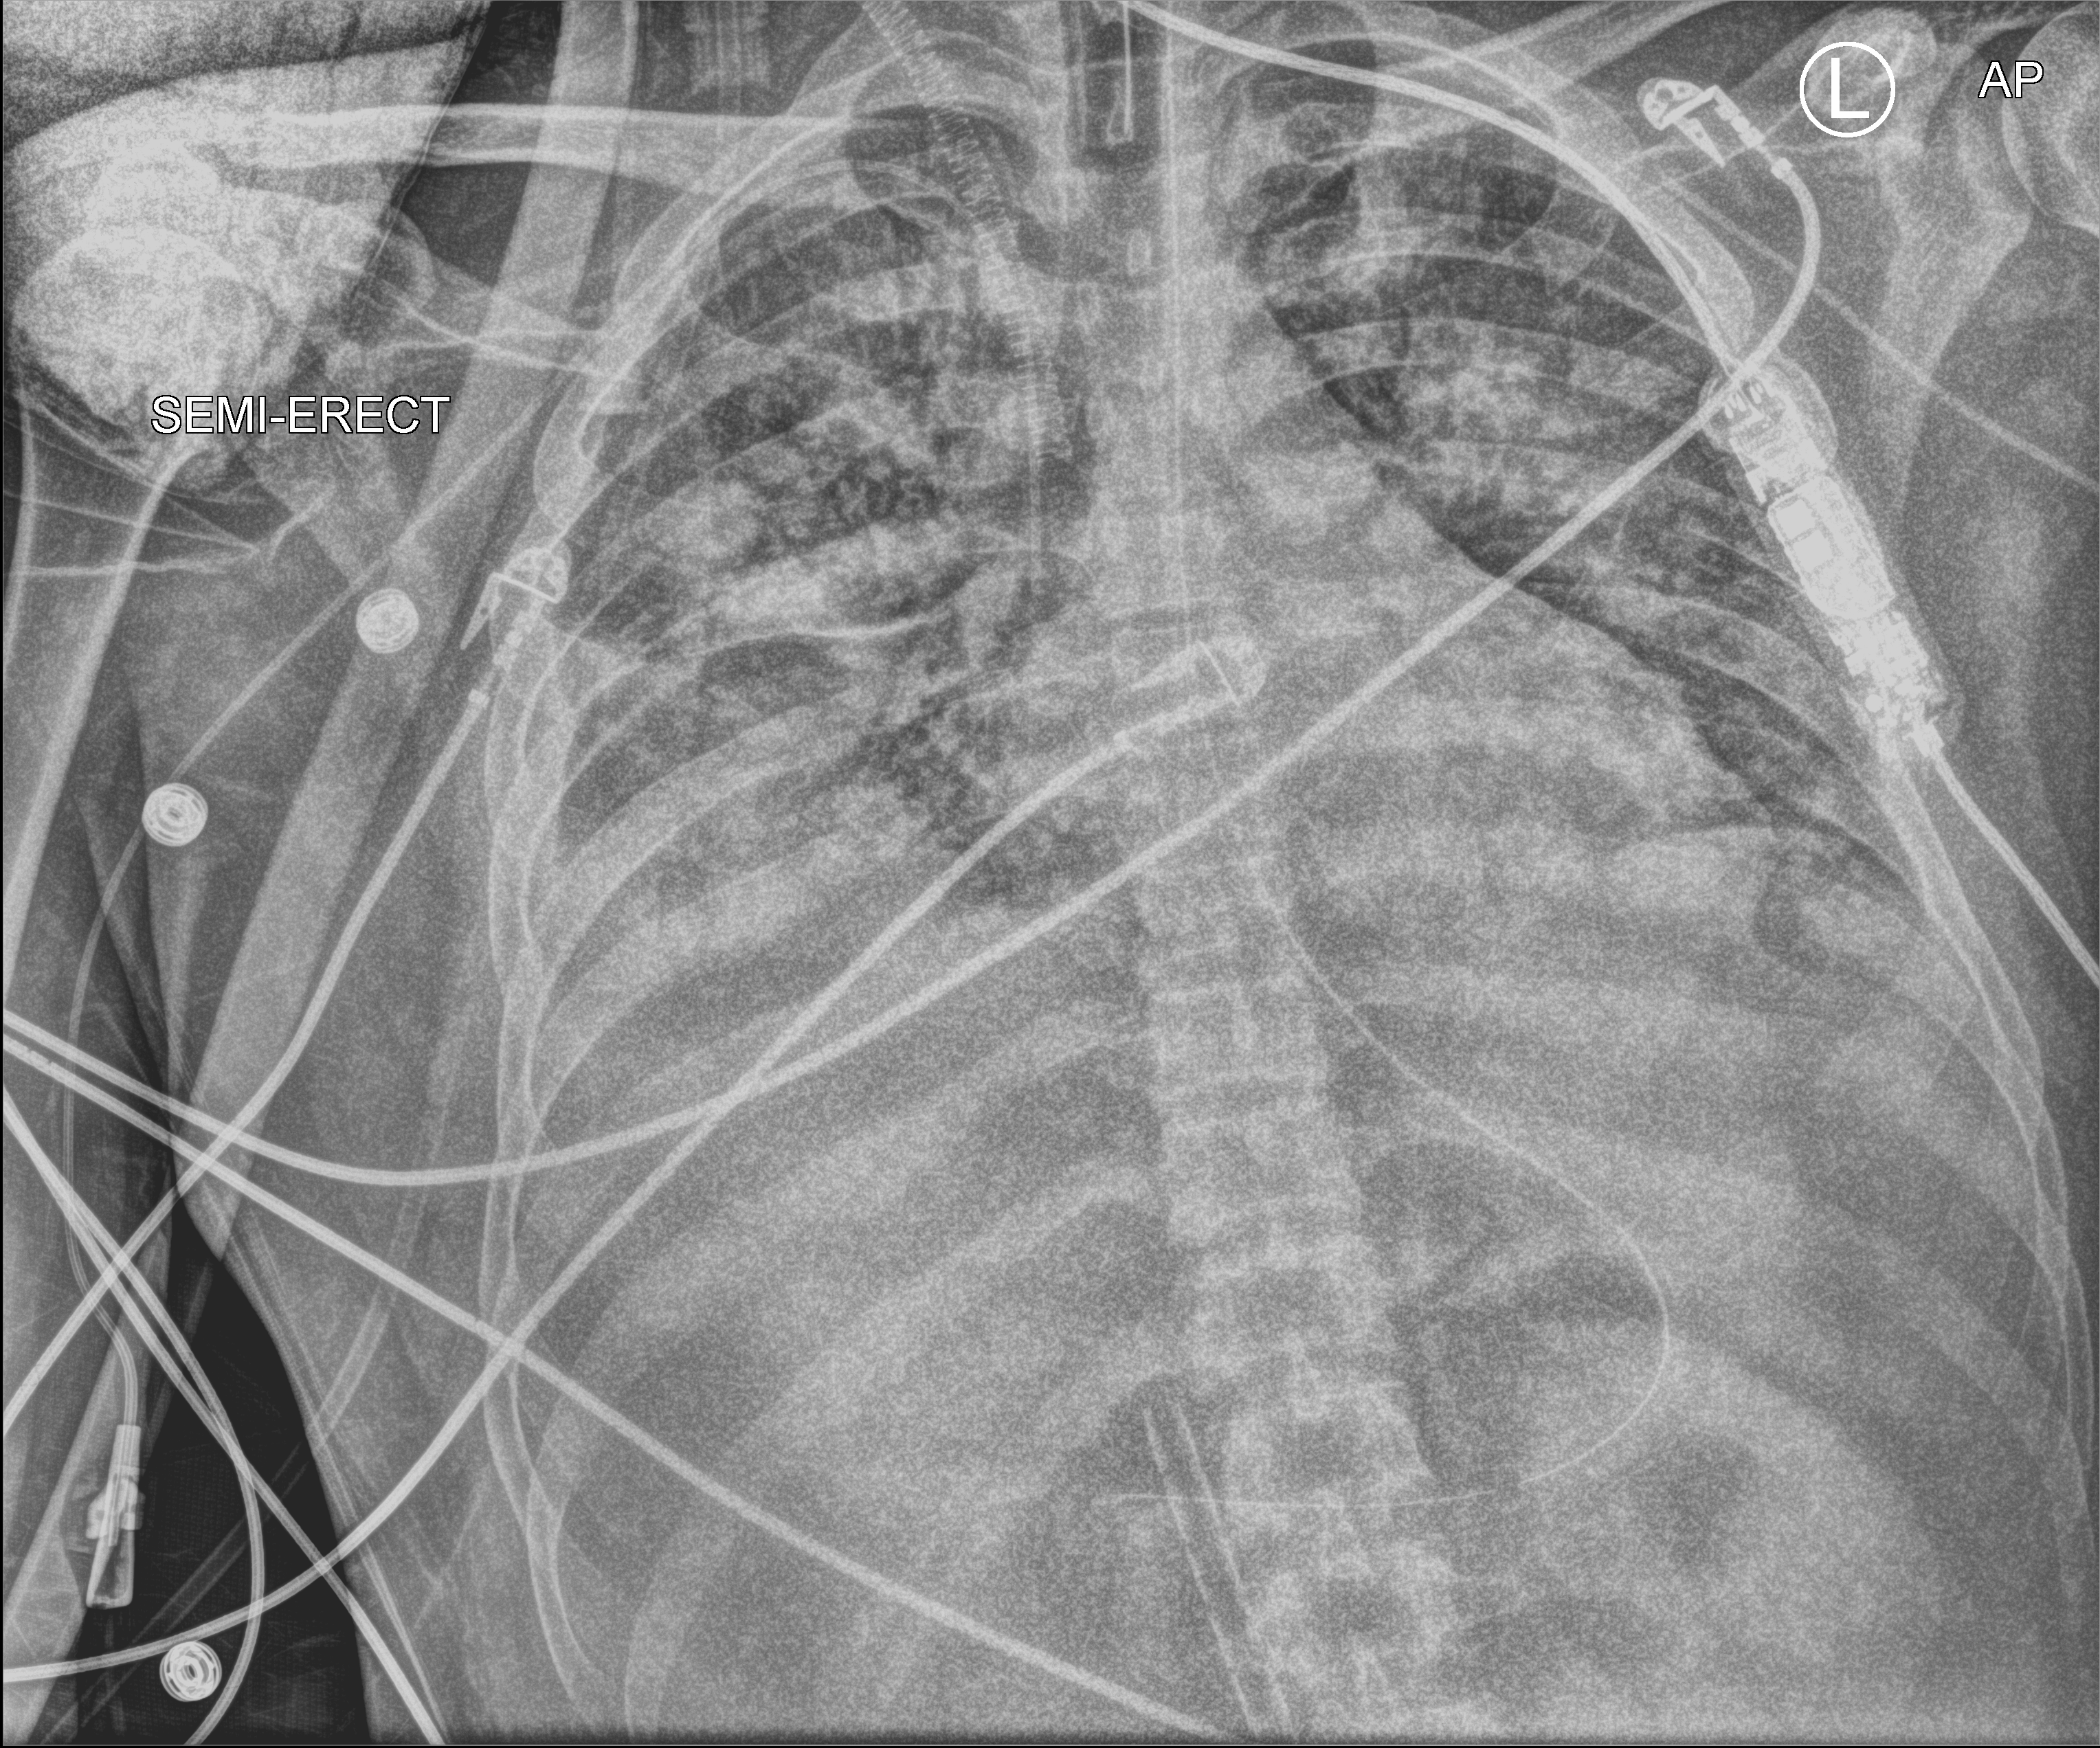
Portable chest radiograph; anteroposterior (AP) projection. Patient hospitalised with COVID-19, aged 18–59 years.
Hospital-stay facts (about this admission, not read from this image; timing relative to this image not recorded): admitted to intensive care during this hospital stay: yes; mechanically ventilated during this hospital stay: yes.